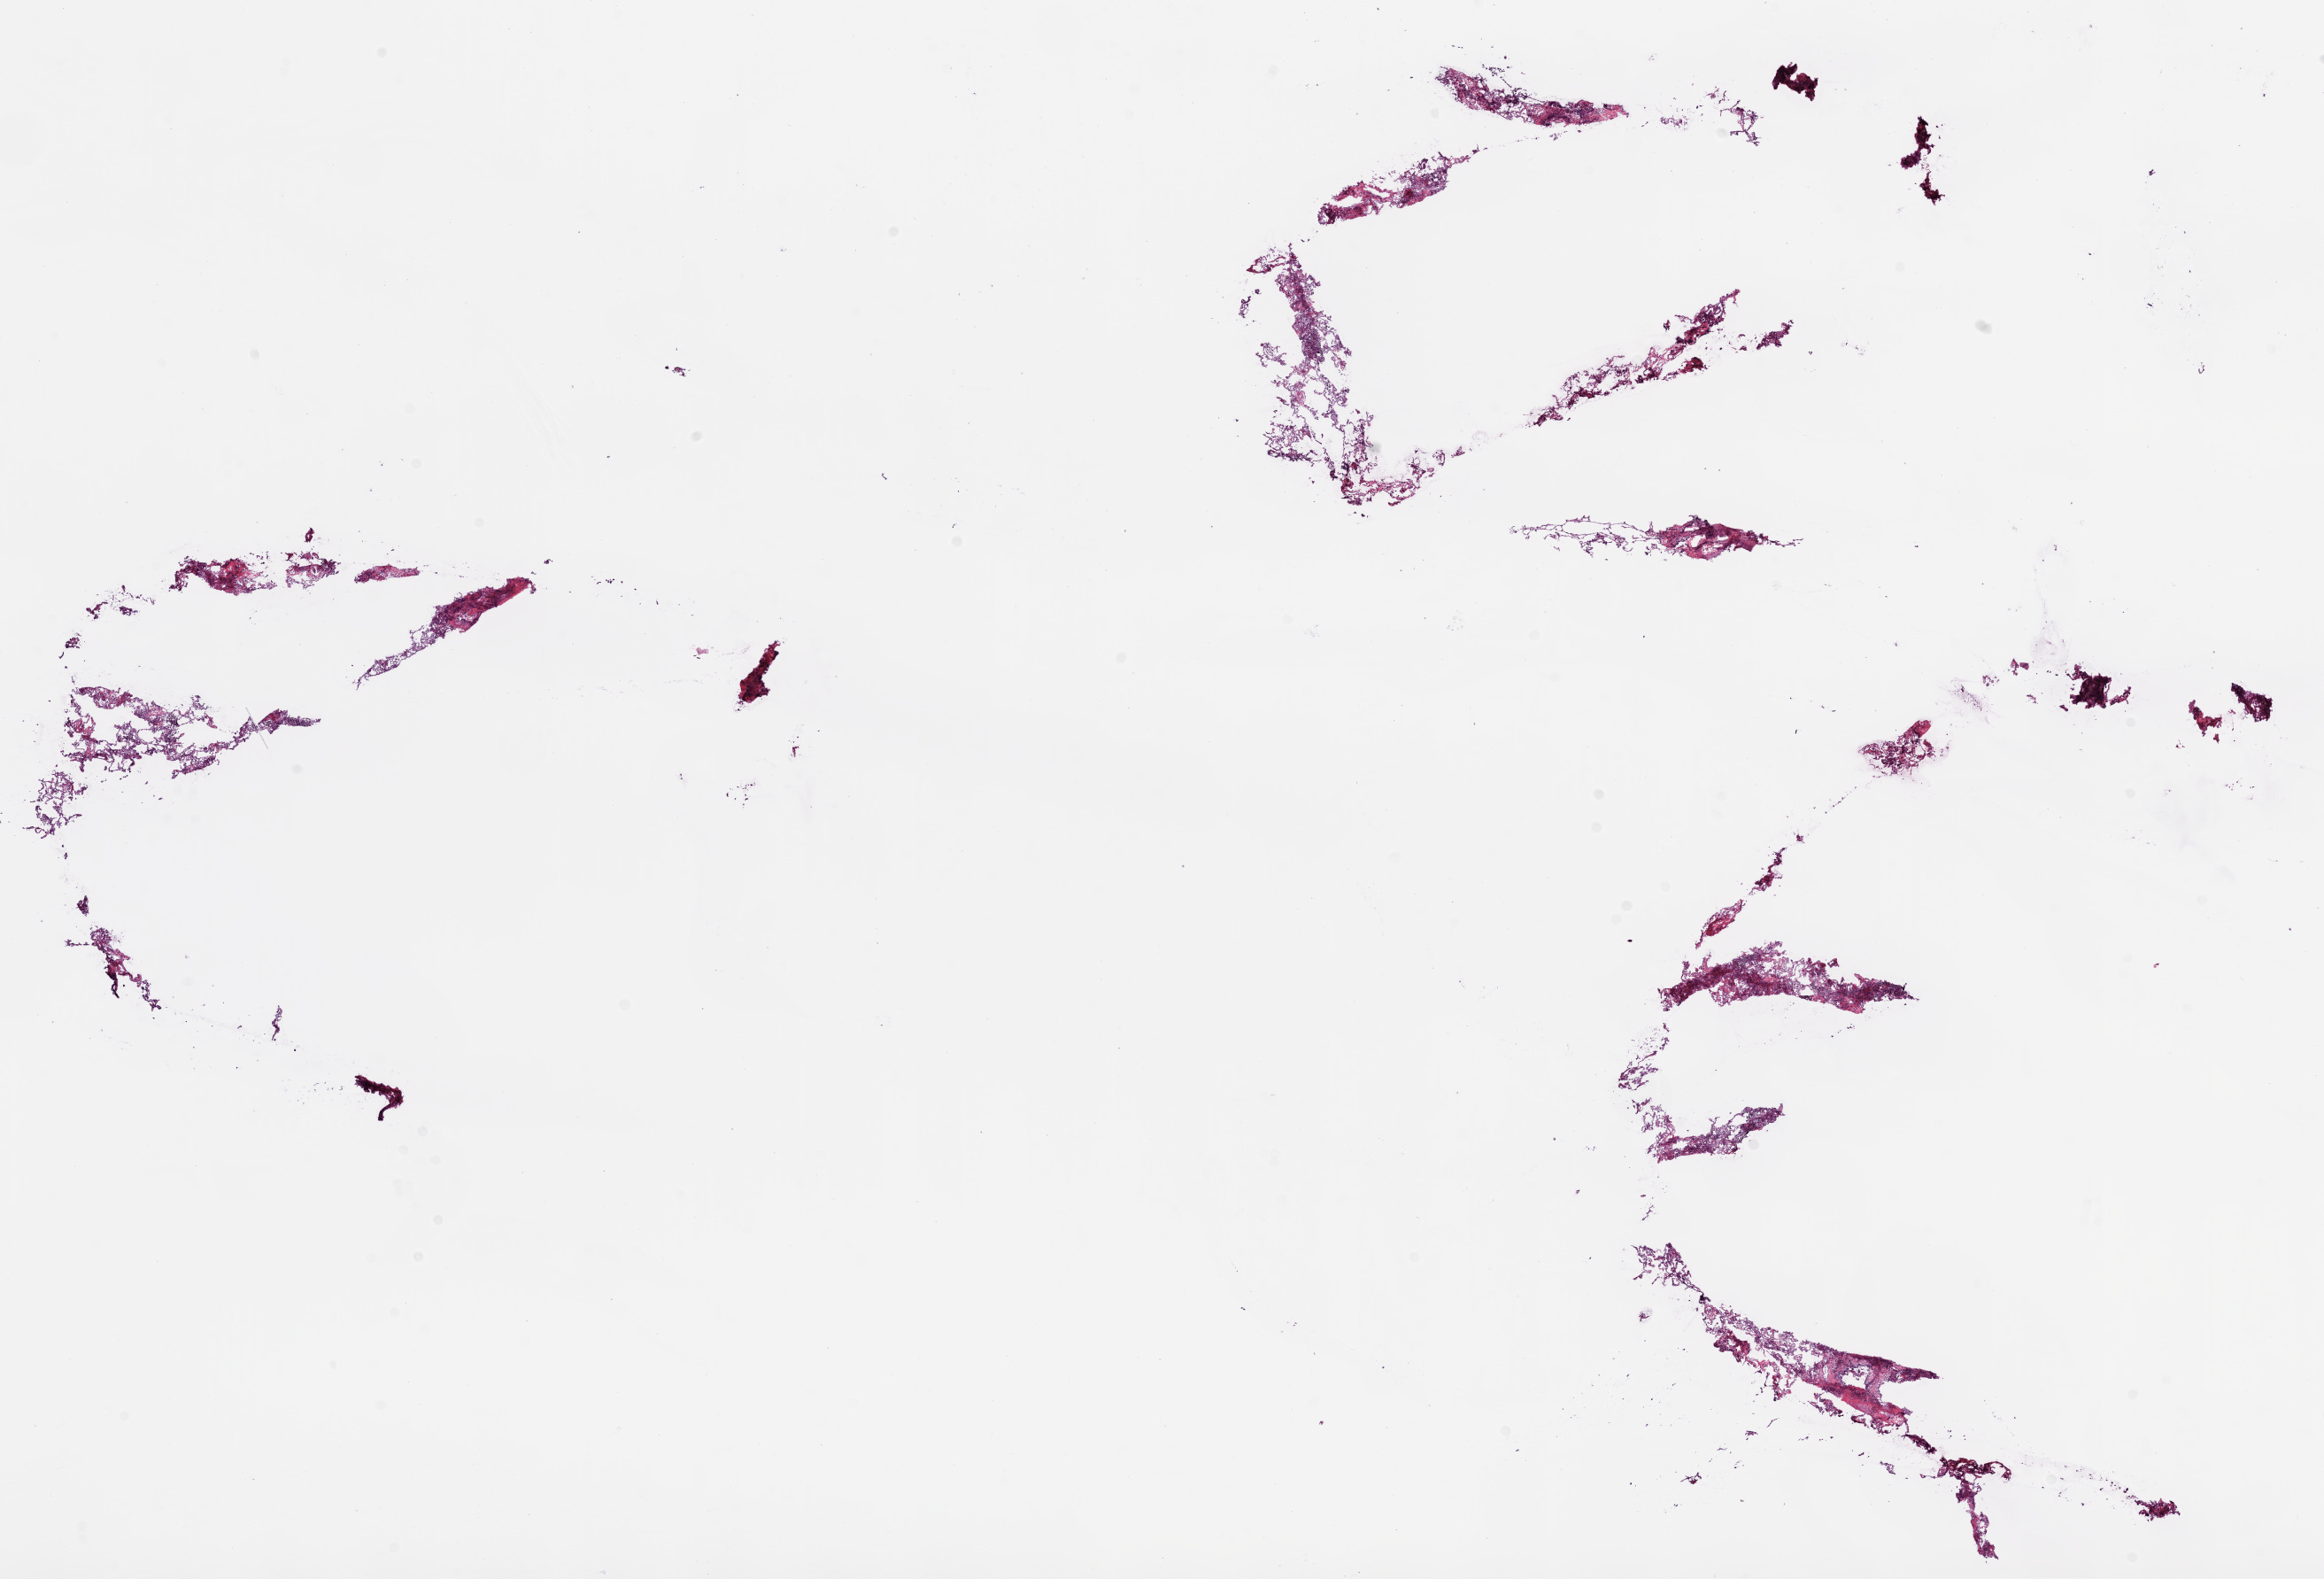
Digitized Hematoxylin and eosin (H&E) stained tissue section (whole slide) — a low-resolution overview of the entire scanned area, about 21.1 x 14.3 mm (acquisition: 20x scan). Frozen section from the bottom of the tissue portion. Solid tissue normal (non-tumour tissue) sample from the lung. Female, age 60 years at initial diagnosis.
* this section: solid tissue normal (non-tumour) sample from the same patient
* patient diagnosis: Squamous cell carcinoma, NOS (lower lobe, lung)